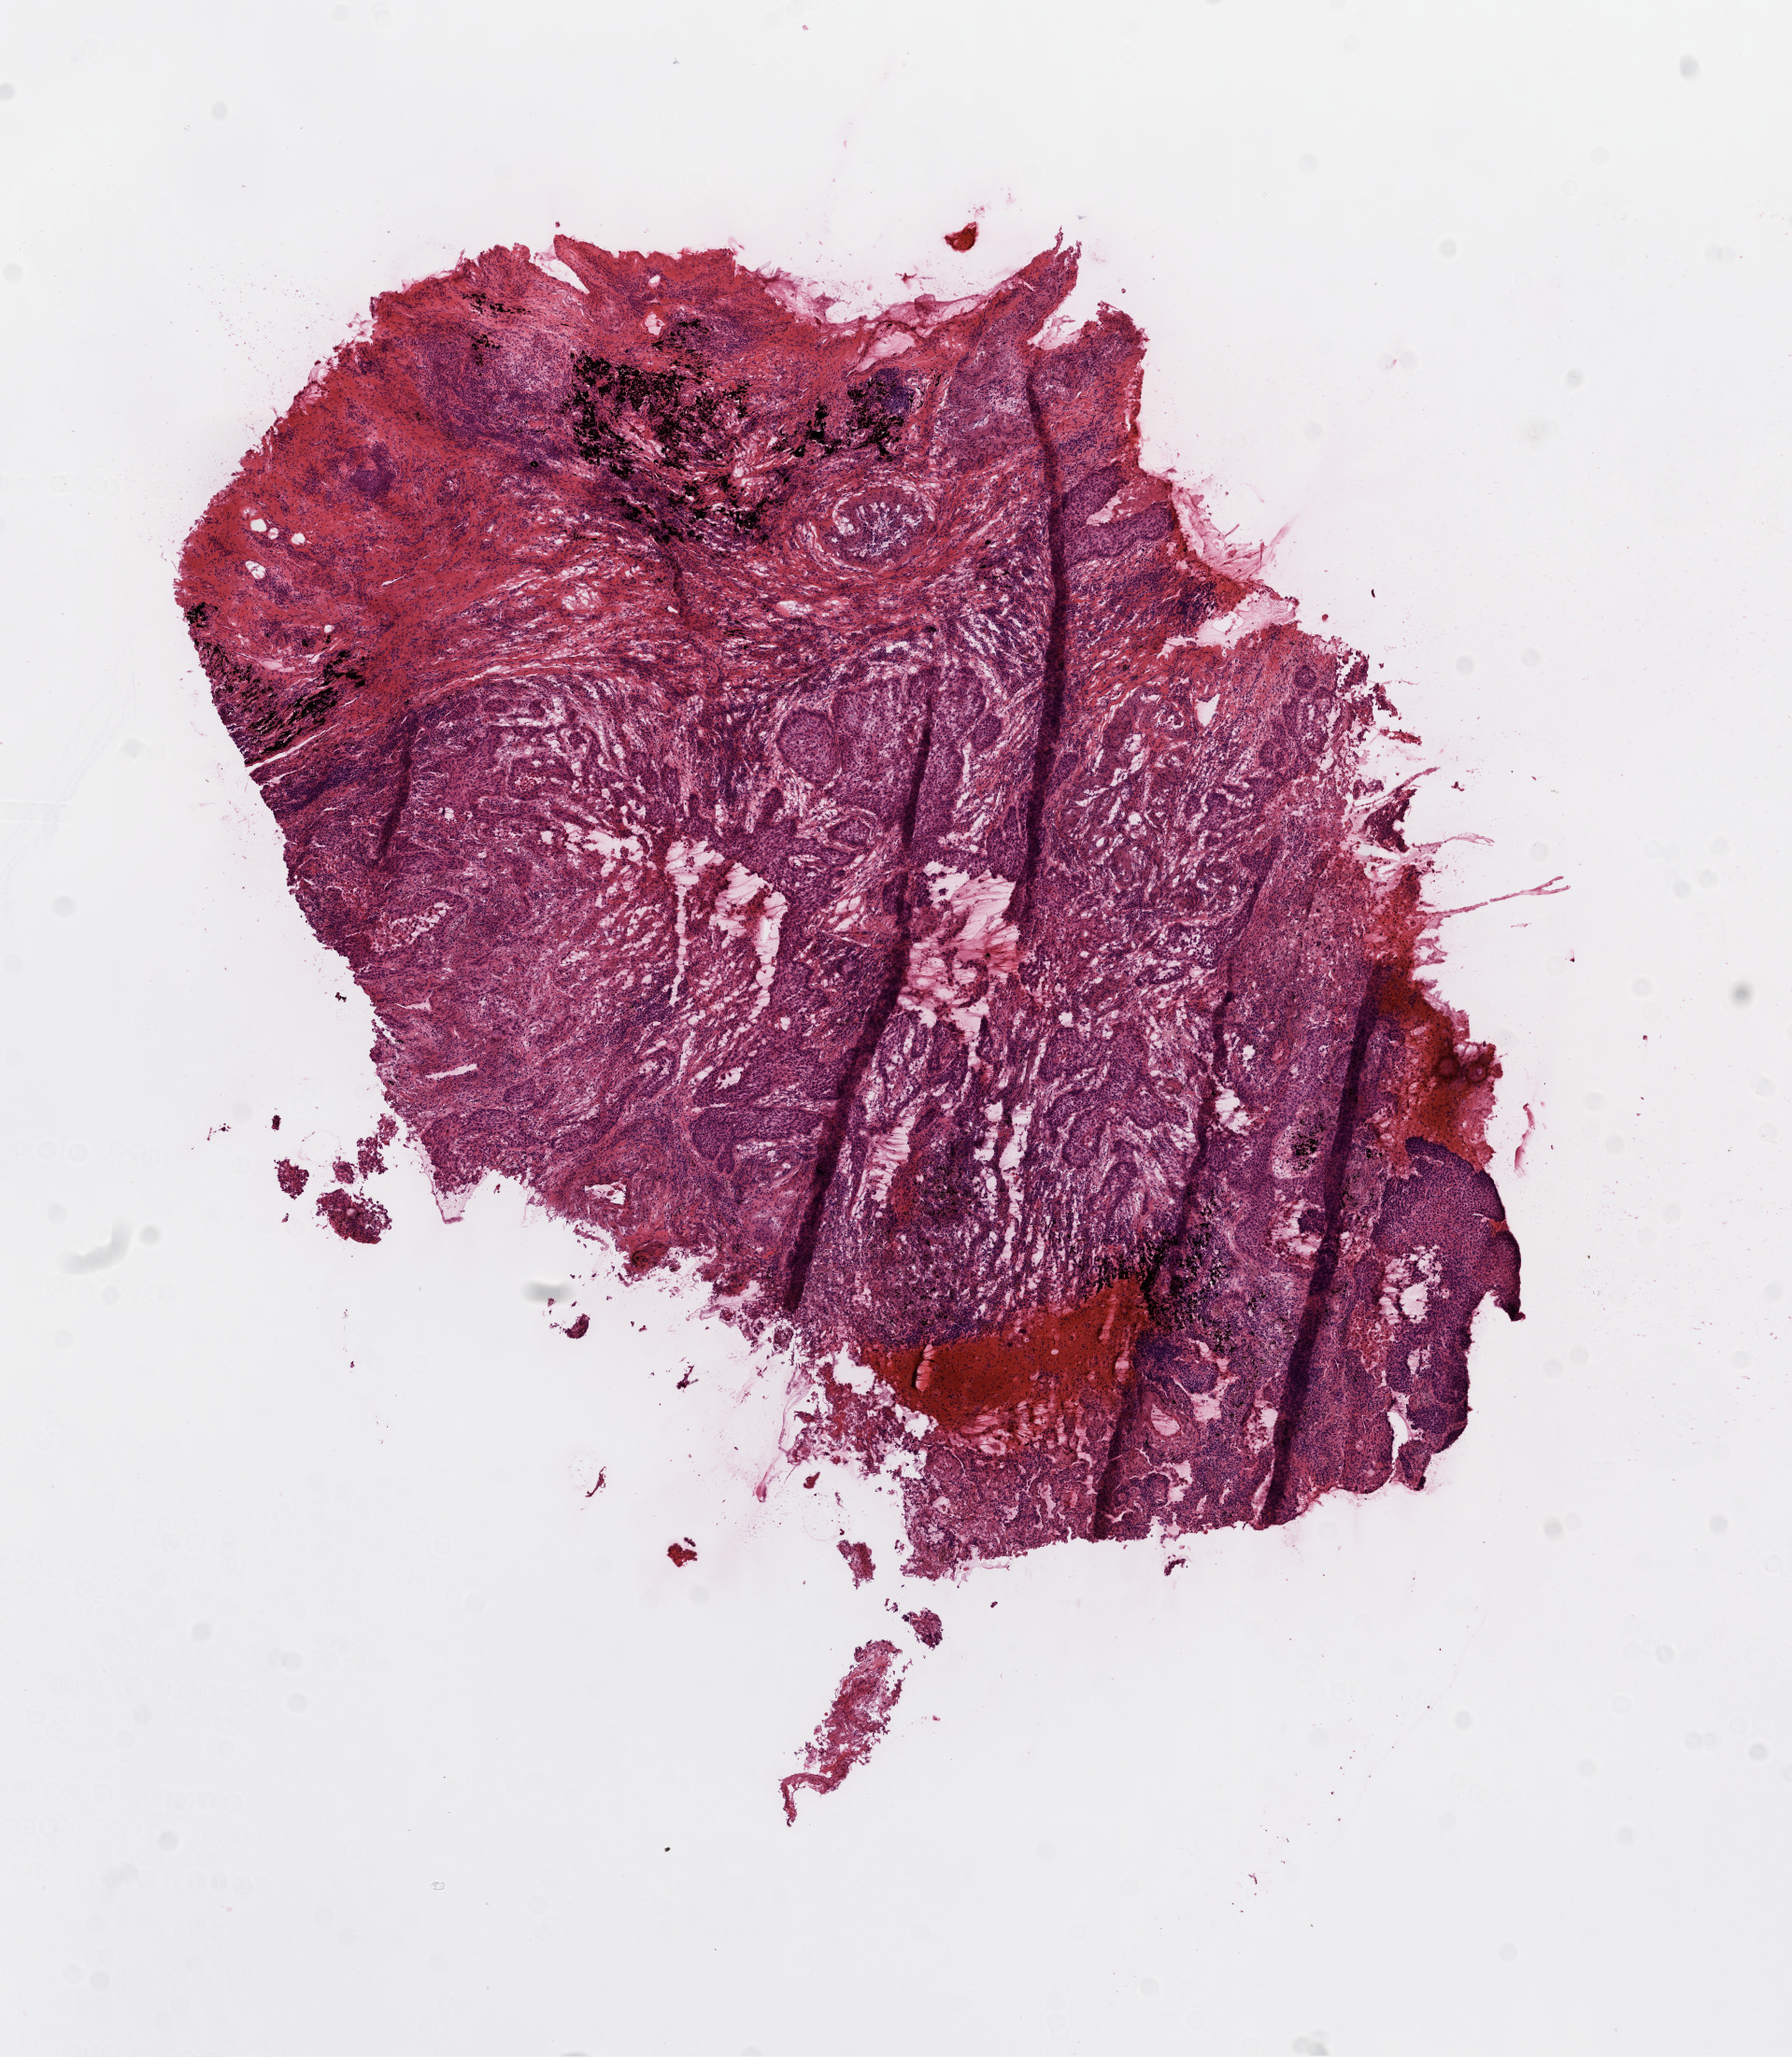
H&E-stained whole-slide image, low-resolution overview of the scanned area, about 7.7 x 8.9 mm, frozen section from the top of the tissue portion, lung, primary tumour sample. Male patient; age at initial diagnosis 64 years.
Pathologic diagnosis: Squamous cell carcinoma, NOS (upper lobe, lung).